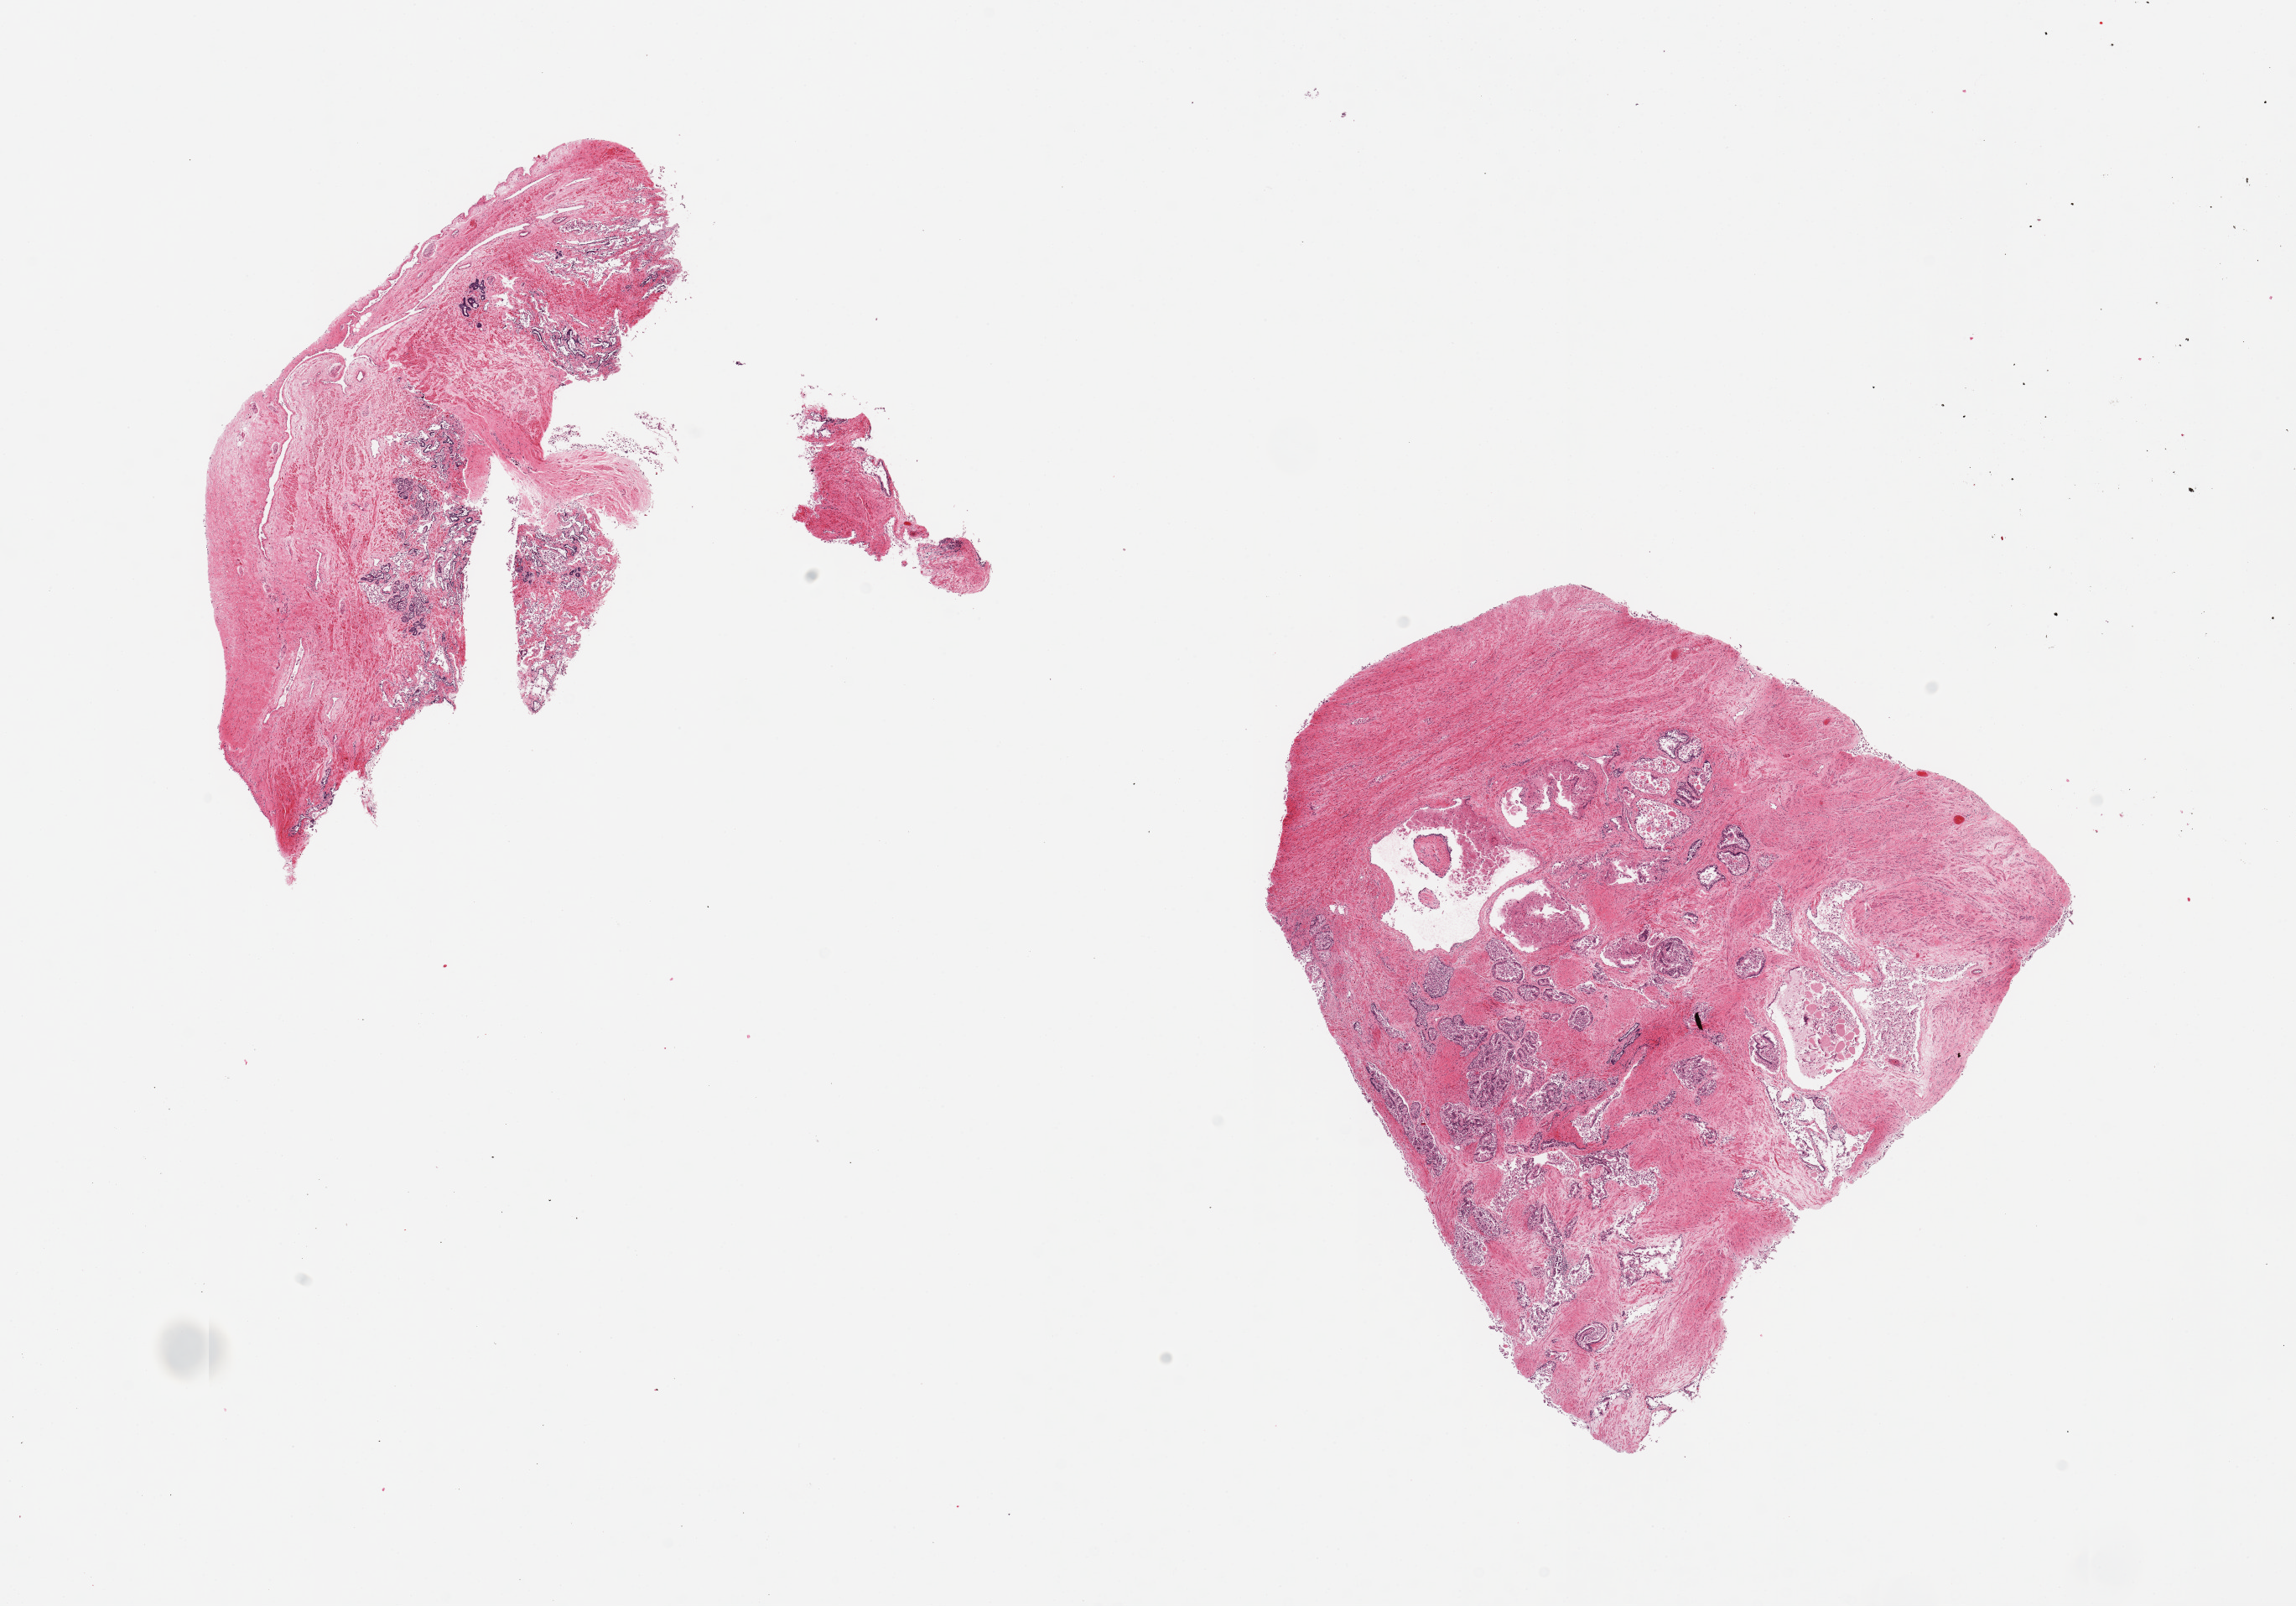
Digitized H&E-stained section, shown as a low-resolution overview of the whole scanned area (about 21.7 x 15.1 mm, slide scanned at 20x); PAXgene-fixed paraffin-embedded (PFPE) section; section of prostate (target tissue); donor tissue sample. Male donor.
Review note (as recorded): 2 pieces; fibromuscular stroma and sloughed glandular epithelium.